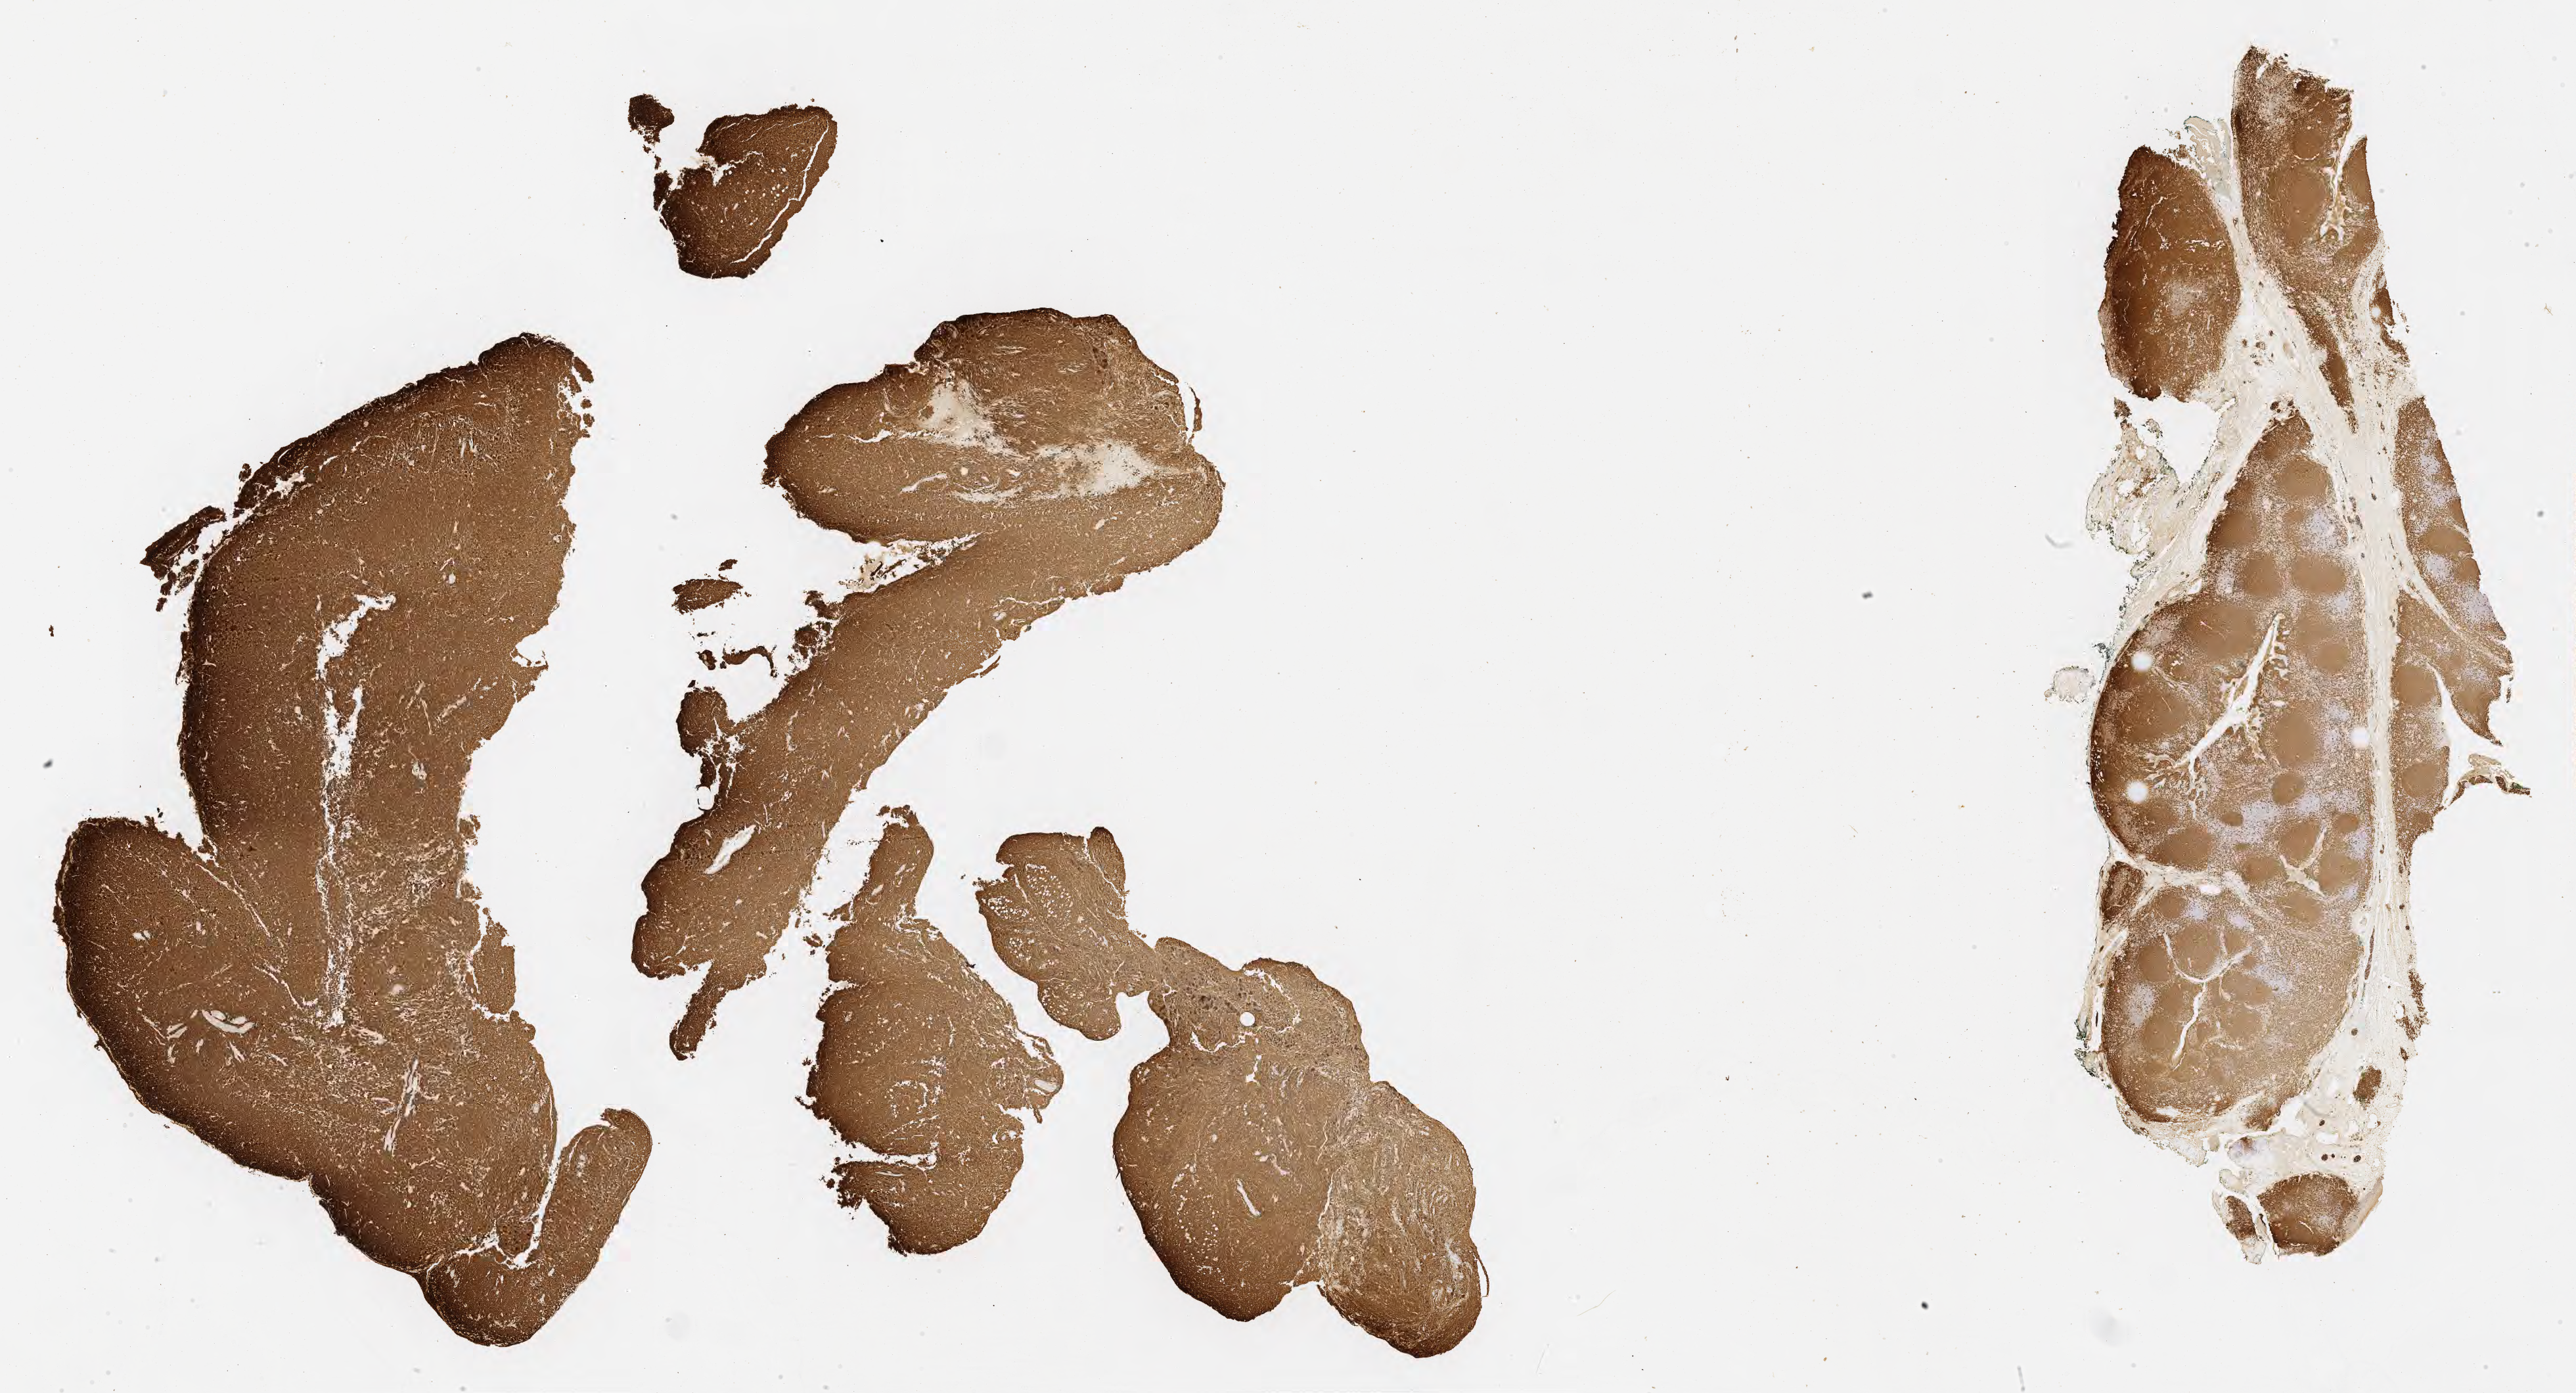
Whole-slide image, immunohistochemical stain for CD20 — whole scanned area (about 31.7 x 17.1 mm) shown as a low-resolution overview, specimen: tumor tissue, site: abdomen proper. Male, age 5 years at initial diagnosis.
Histologic diagnosis: Burkitt lymphoma, NOS.